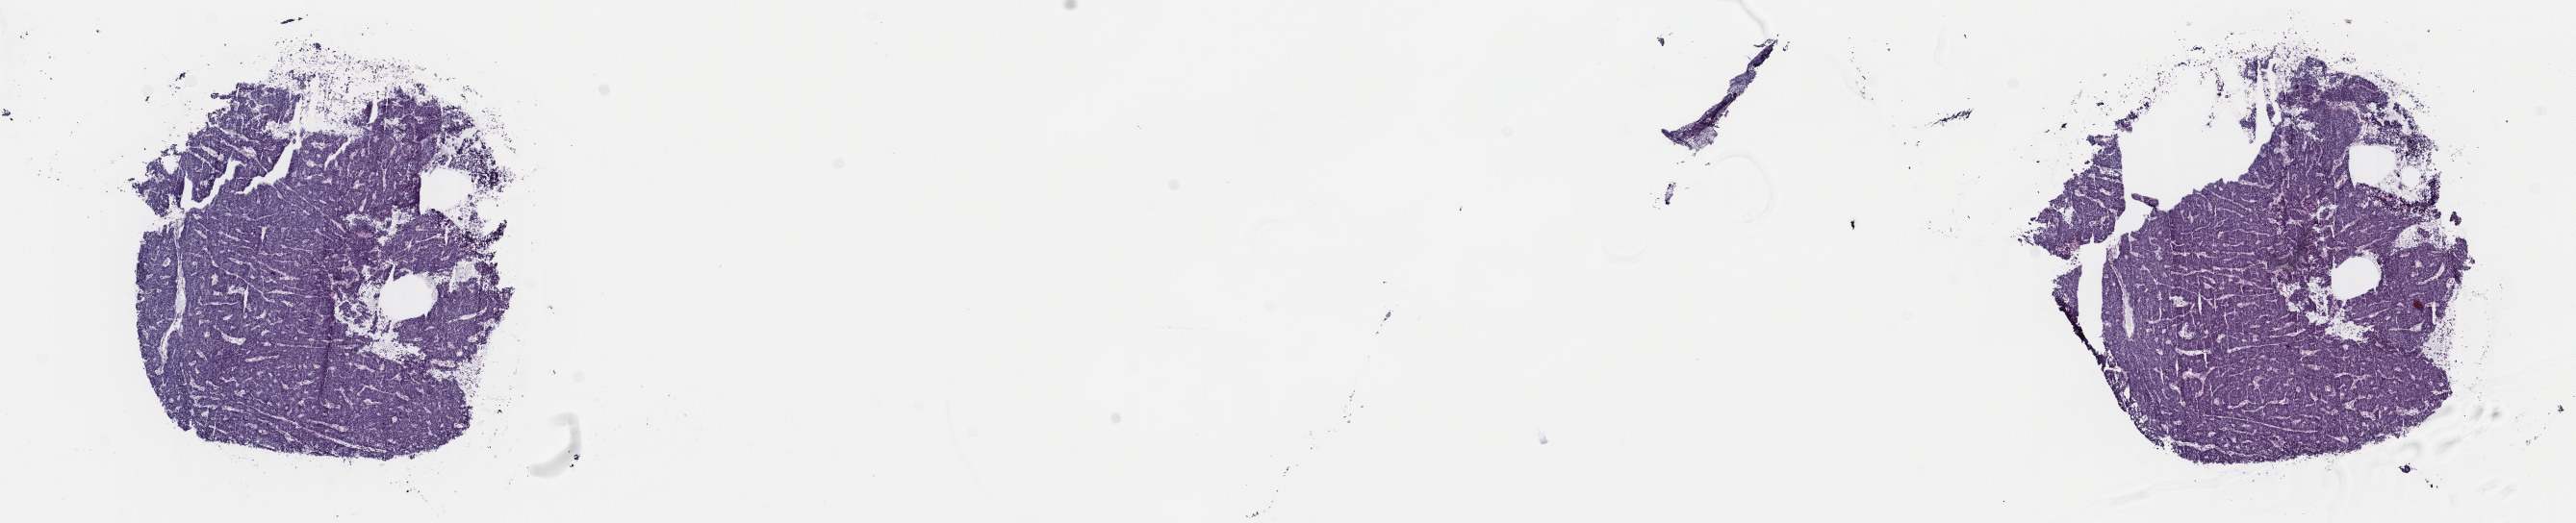
H&E whole-slide image — low-resolution overview of the scanned area, about 21.1 x 4.3 mm; frozen section from the top of the tissue portion; uterus, primary tumour sample. Patient: female, age at initial diagnosis 75 years. Histologic grade: G3 (poorly differentiated). Slide review estimates, as recorded: tumour cells 100%, tumour nuclei 80%, normal cells 0%, stromal cells 0%, necrosis 0%. Inflammatory infiltration, as recorded: lymphocyte infiltration 2%, monocyte infiltration 2%, neutrophil infiltration 0%.
Diagnosis: Endometrioid adenocarcinoma, NOS (endometrium). FIGO stage: IA.